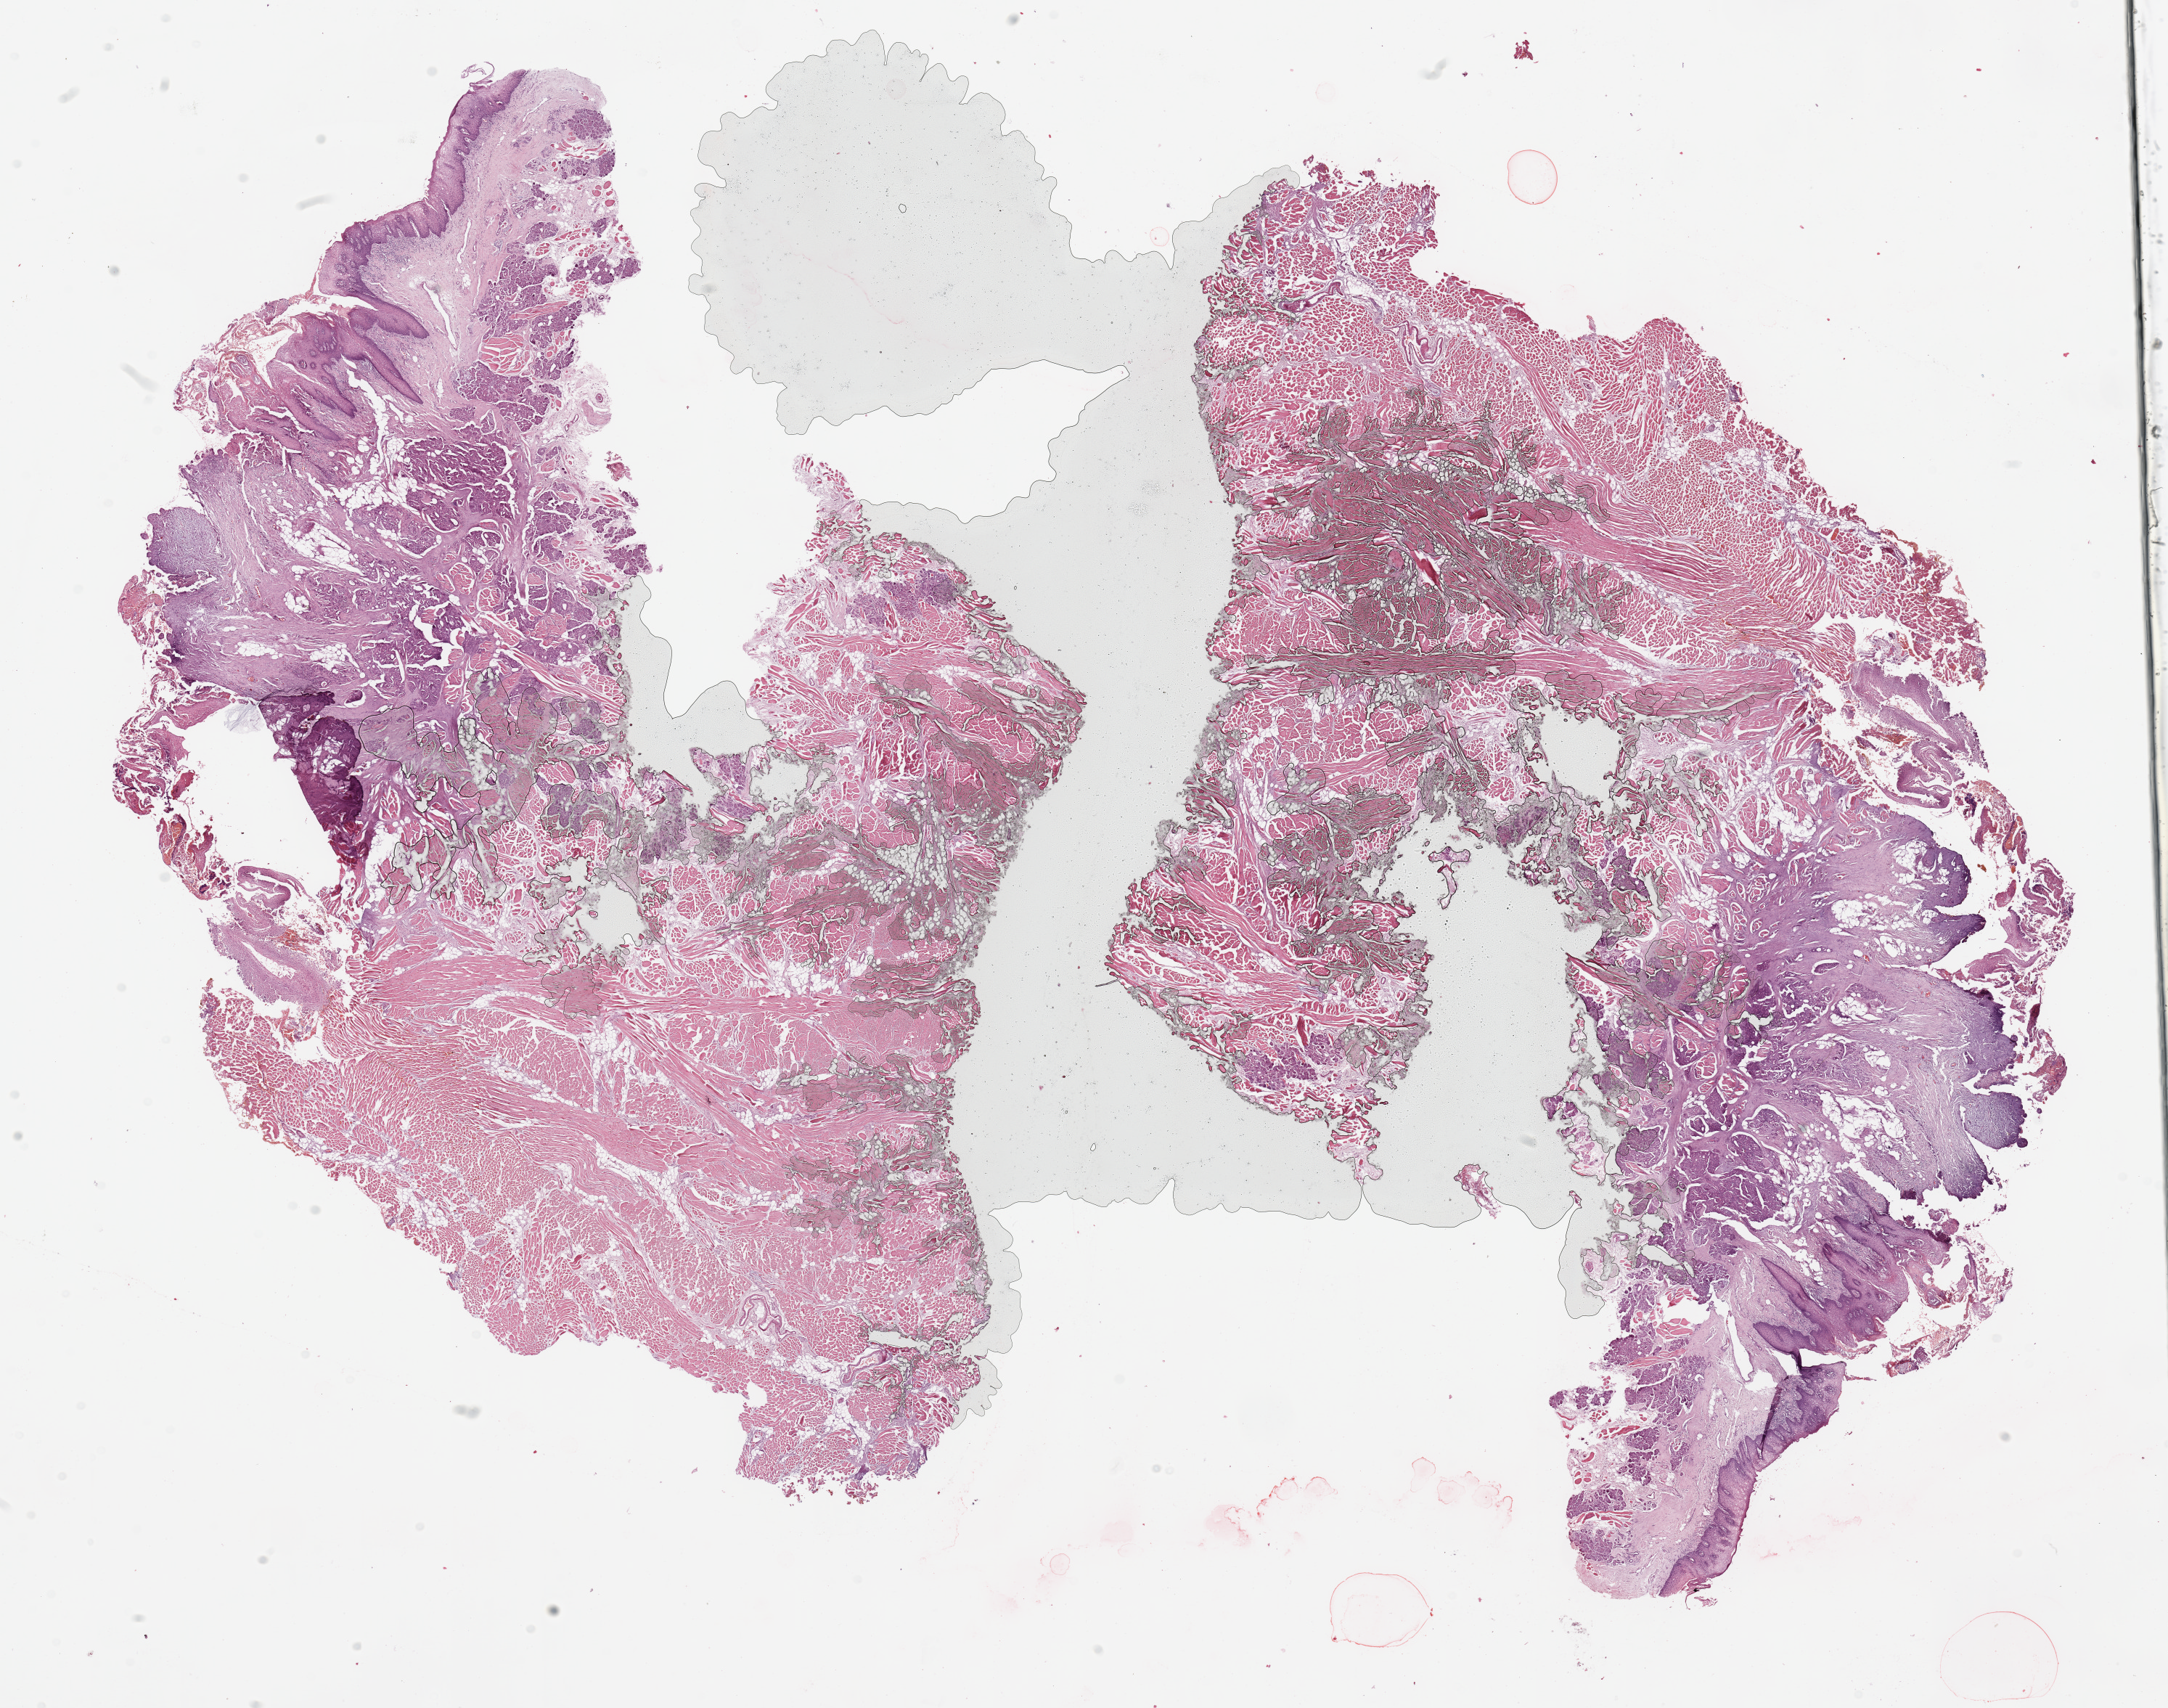
H&E whole-slide image, a low-resolution overview of the entire scanned area, about 23.6 x 18.6 mm, normal (non-tumour) tissue sample, sampled site: tongue. Patient: male, age 54 years.
This section: normal (non-tumour) tissue from the same patient. Patient diagnosis: Squamous cell carcinoma, NOS (tongue, NOS).